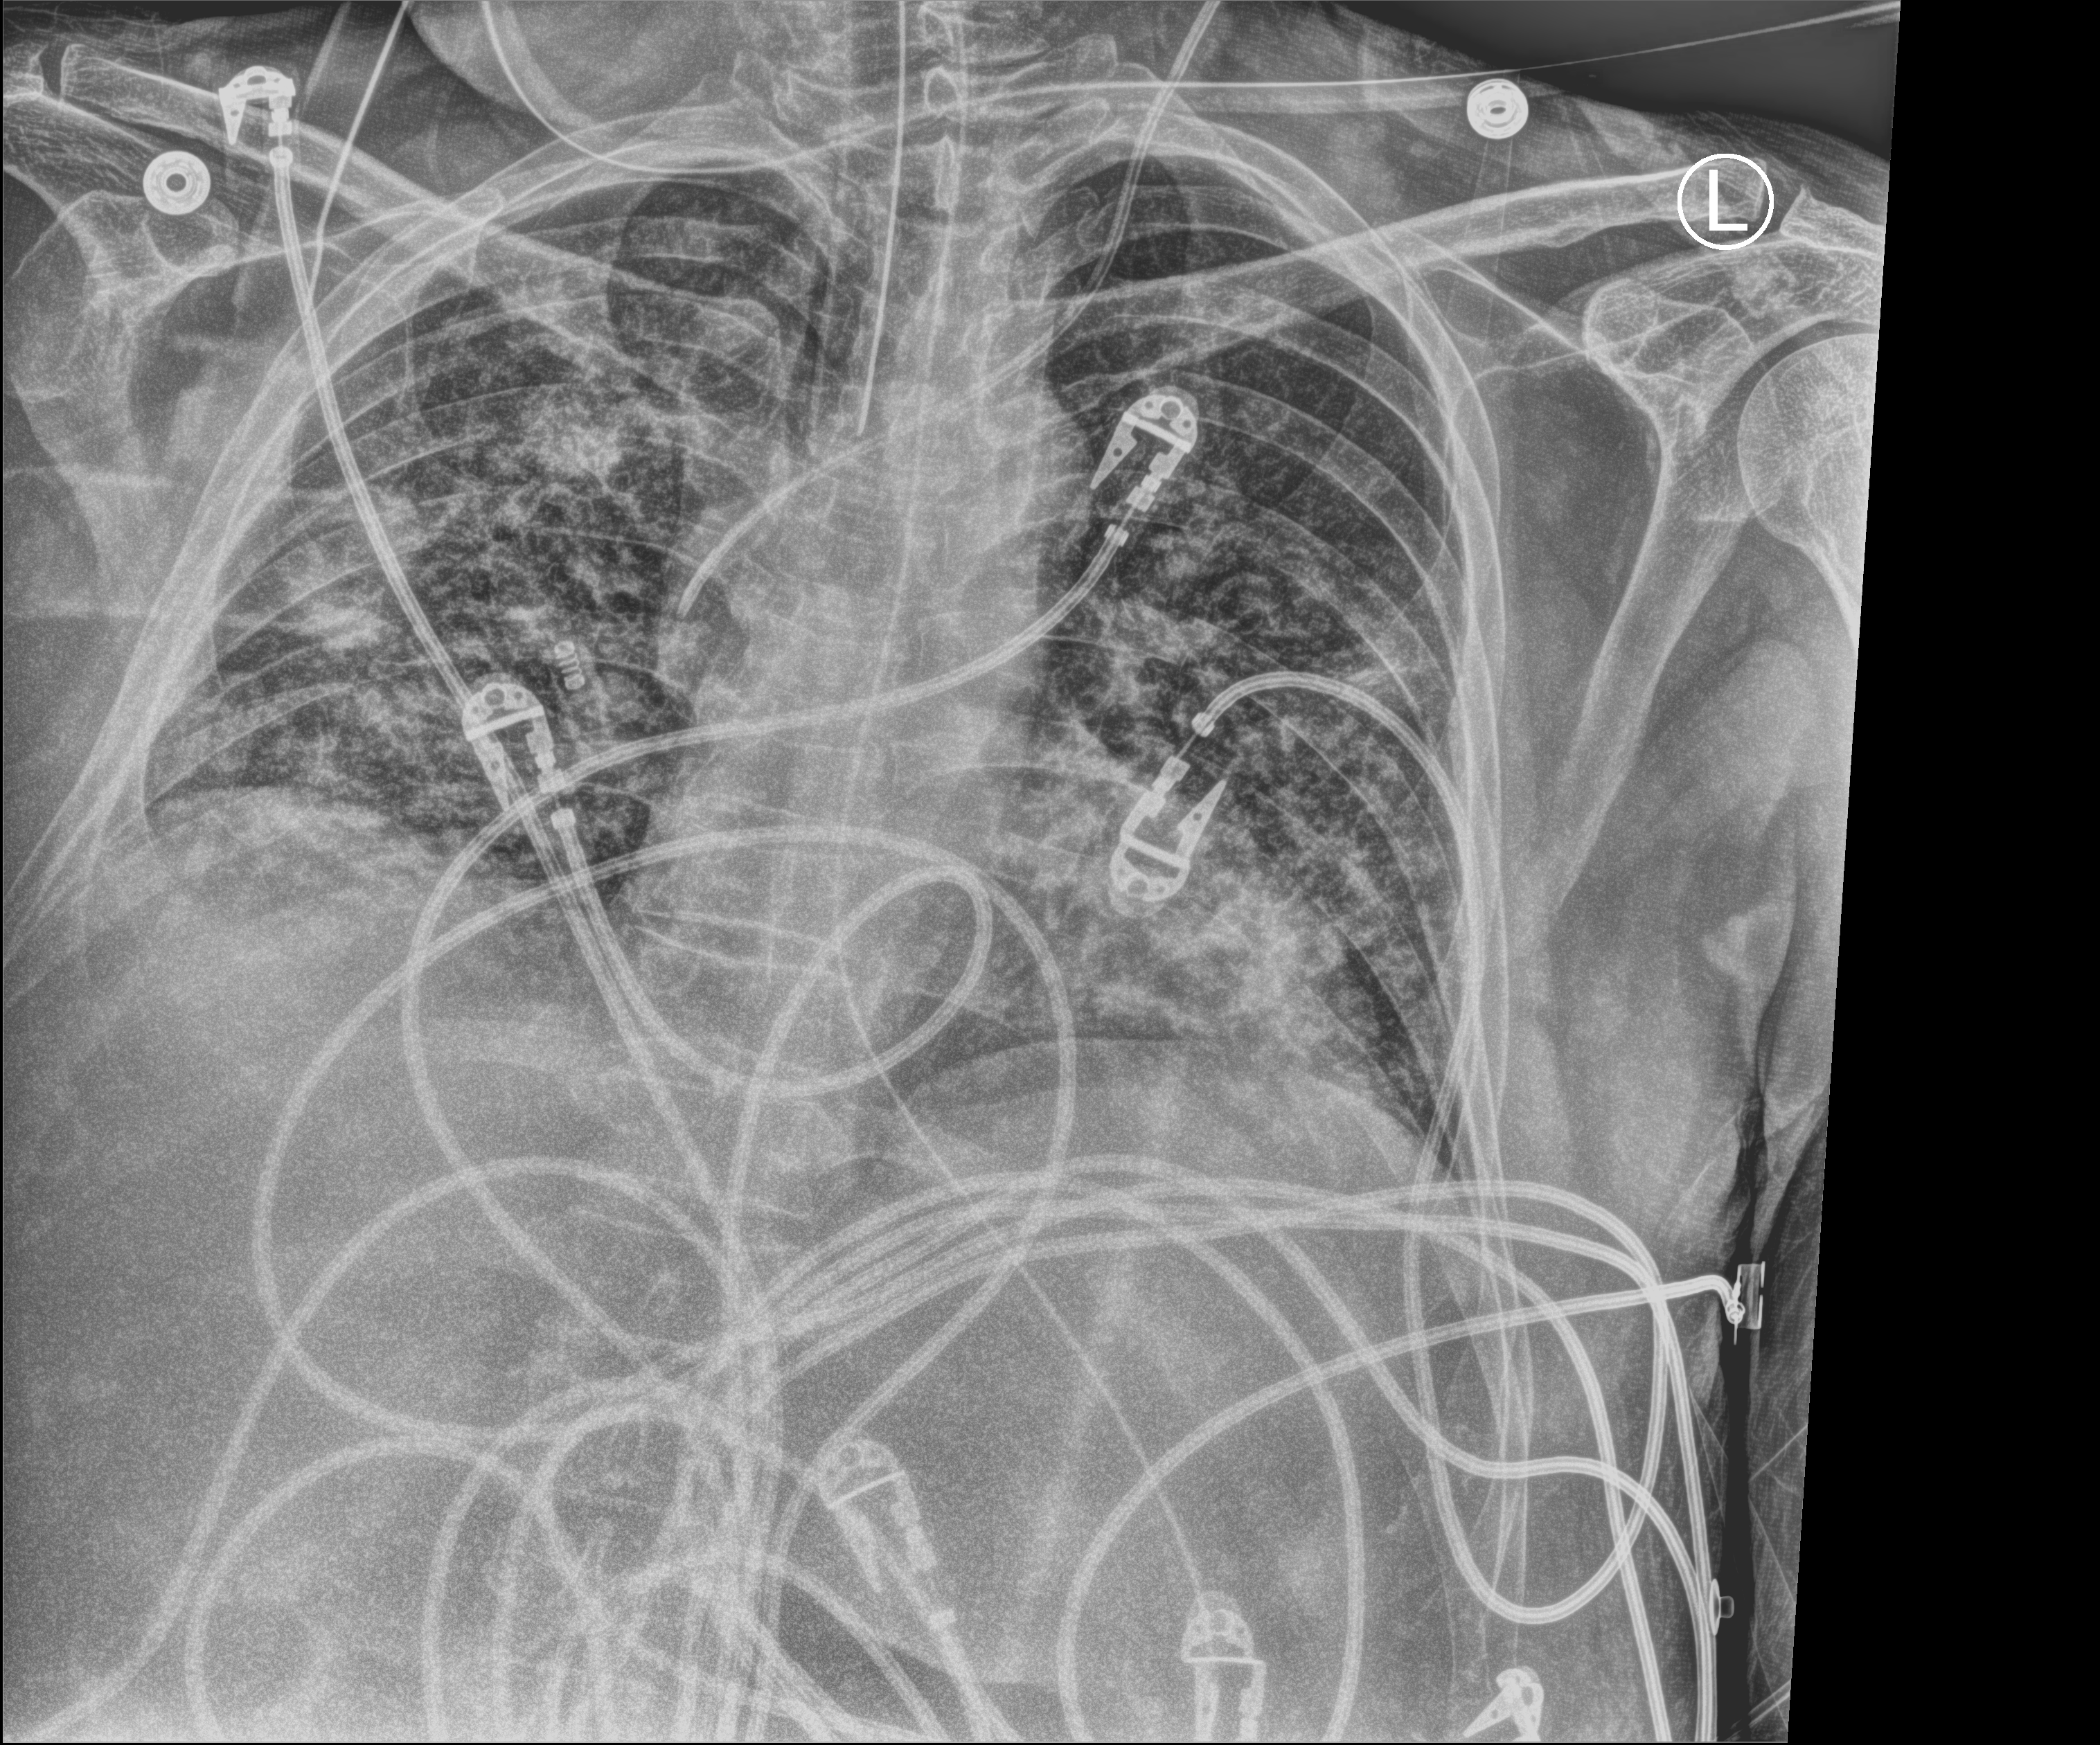
Chest X-ray (portable); anteroposterior (AP) projection. Male patient hospitalised with COVID-19, age 60–74 years.
Admission-level facts for this patient (not findings on this image; timing relative to this image not recorded):
- admitted to intensive care during this hospital stay: yes
- hypertension (admission record): no